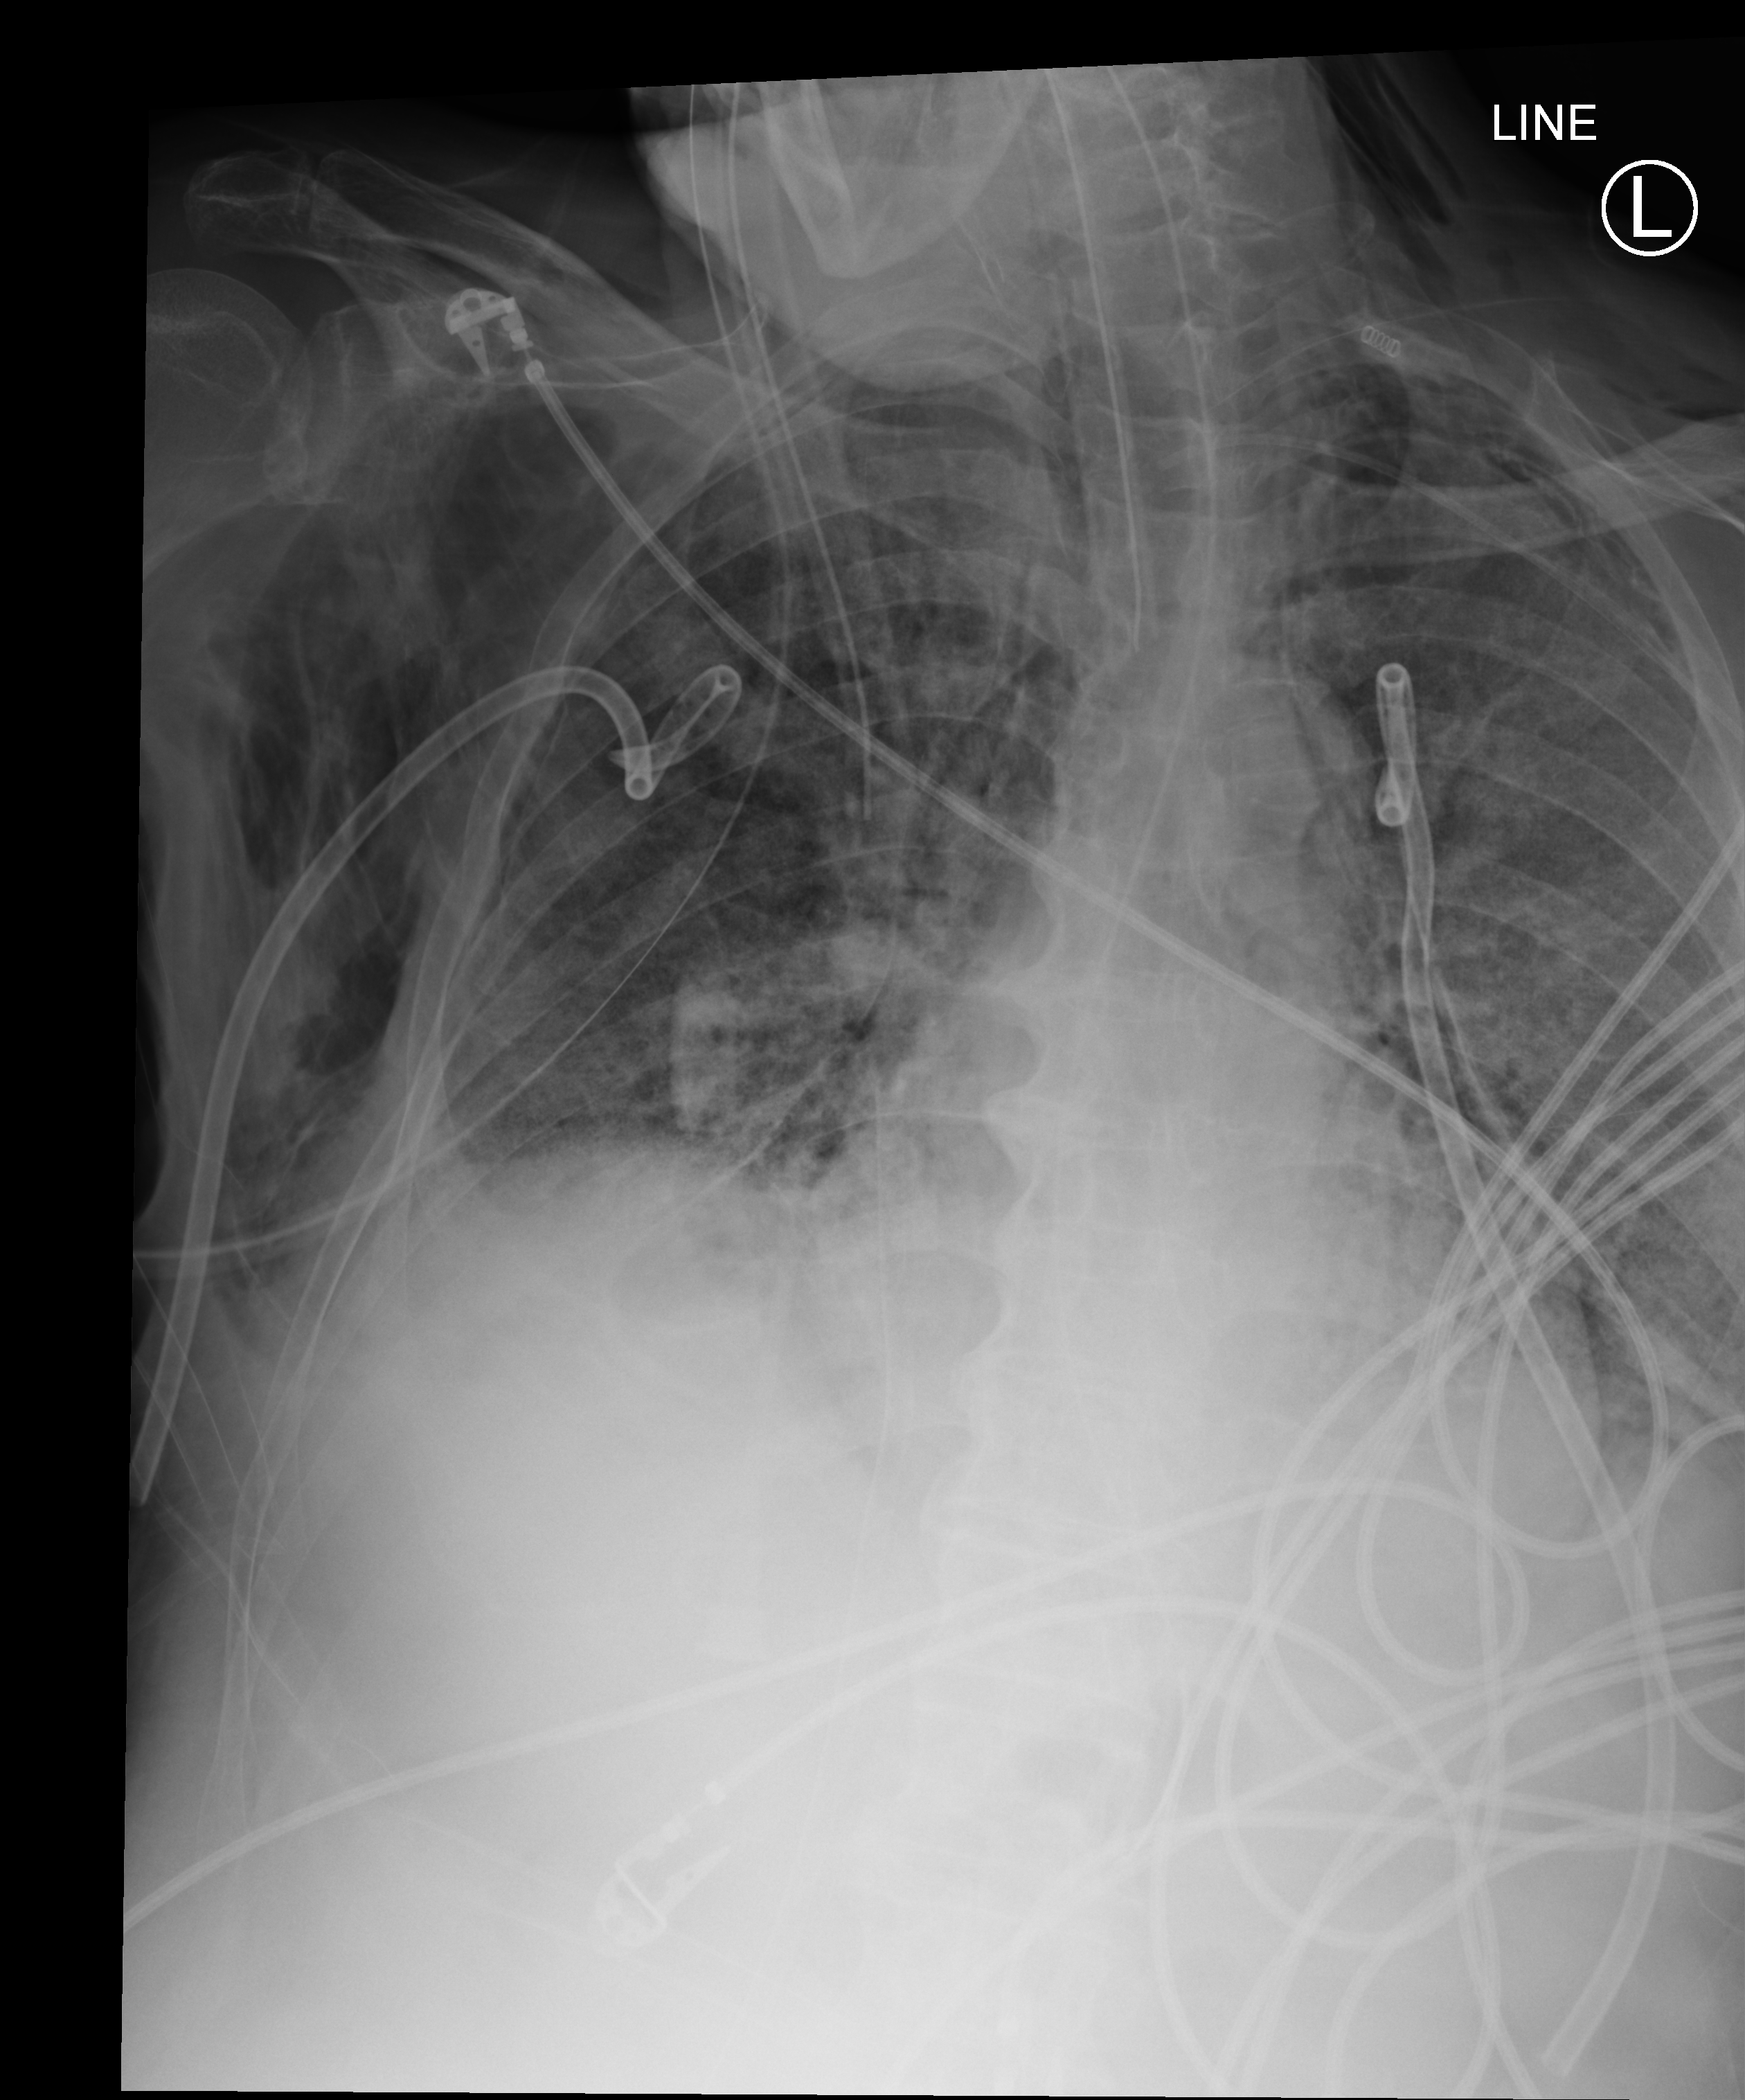
Chest X-ray (portable); anteroposterior (AP) projection. Male patient hospitalised with COVID-19, age 75–90 years.
Admission-level facts for this patient (not findings on this image; timing relative to this image not recorded): mechanically ventilated during this hospital stay: yes.